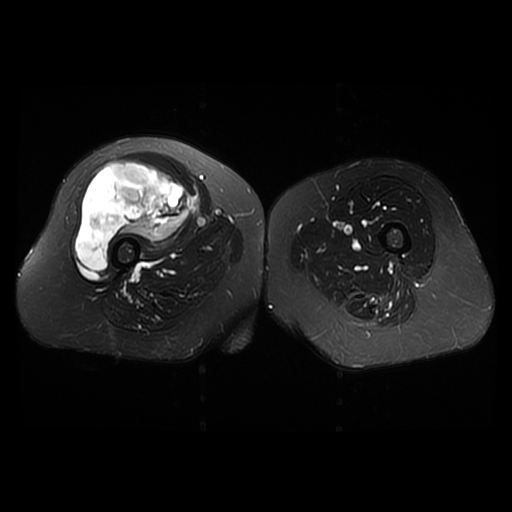
MRI of an extremity soft-tissue mass, one axial slice; slice 24 of 42 in the series (ordered by position); T2-weighted fat-saturated; 512 × 512 image matrix, field of view 440 × 440 mm. Female patient. Case-level facts recorded for this patient, not image findings: histological type: pleiomorphic undifferentiated sarcoma; grade: high; site of the primary tumour: right quadricep.
Annotated regions visible in this slice (manually delineated by an expert):
- gross tumour volume including surrounding oedema: bounding box (x1, y1, x2, y2) in pixels: (74, 161, 192, 271)
- gross tumour volume (mass): (74, 161, 192, 271)